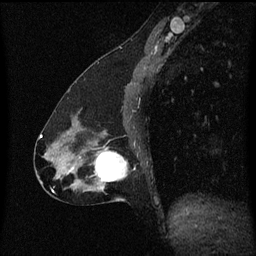
Breast MRI (dynamic contrast-enhanced), one sagittal slice; position 27 of 60 along the scan axis; dynamic contrast-enhanced series, image 2 of 3 at this slice position (ordered by acquisition); 1.5 T; TE 4.2 ms, TR 8.4 ms; 2 mm slice thickness; 256 × 256 image matrix, field of view 200 × 200 mm. Patient: female, 47 years.
Annotated regions visible in this slice (semi-automatic segmentation, software-assisted and operator-edited):
- analysis volume of interest (the breast-tissue region the enhancement analysis was run in; not a lesion): box from (x=81, y=148) to (x=126, y=193) px
- tumour enhancement mask (voxels above the 70 % enhancement threshold inside the analysis volume of interest): (x=95, y=148)–(x=126, y=183)